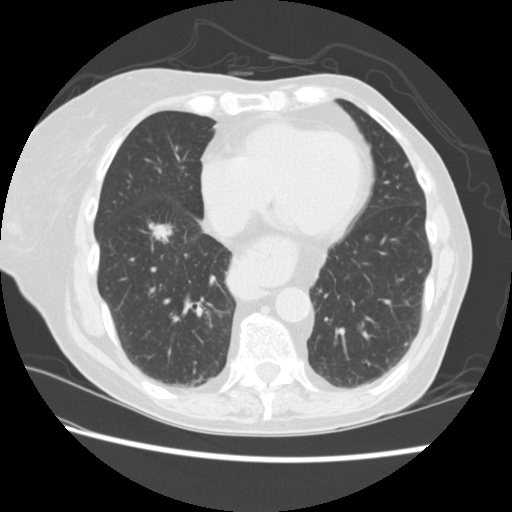
Low-dose screening chest CT, one axial slice. Reconstruction kernel STANDARD. 120 kVp. Lung window (W 1500 / L -600 HU). 512 × 512 image matrix.
Annotated regions visible in this slice (outlined manually by an expert reader):
- lesion 2 (tumor, lower lobe of right lung): bounding box <150,224,172,242> (left, top, right, bottom; pixels)